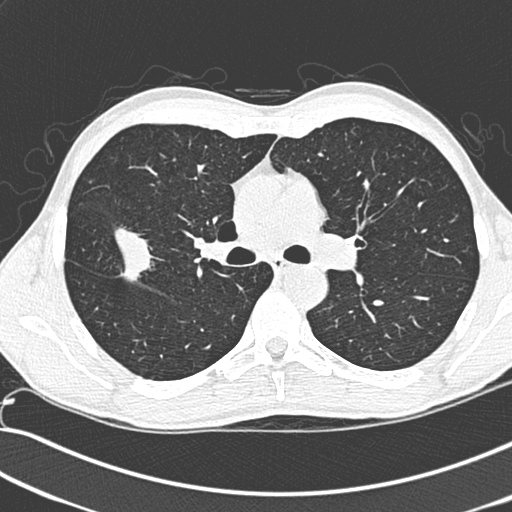
Low-dose screening chest CT, one axial slice; position 187 of 281 along the scan axis; lung window (W 1500 / L -600 HU); 1.3 mm slice thickness; 512 × 512 image matrix, field of view 341 × 341 mm.
Structures marked on this image (expert manual segmentation):
- lesion 1 (tumor, upper lobe of right lung): bounding box (x1, y1, x2, y2) in pixels: (115, 227, 155, 282)